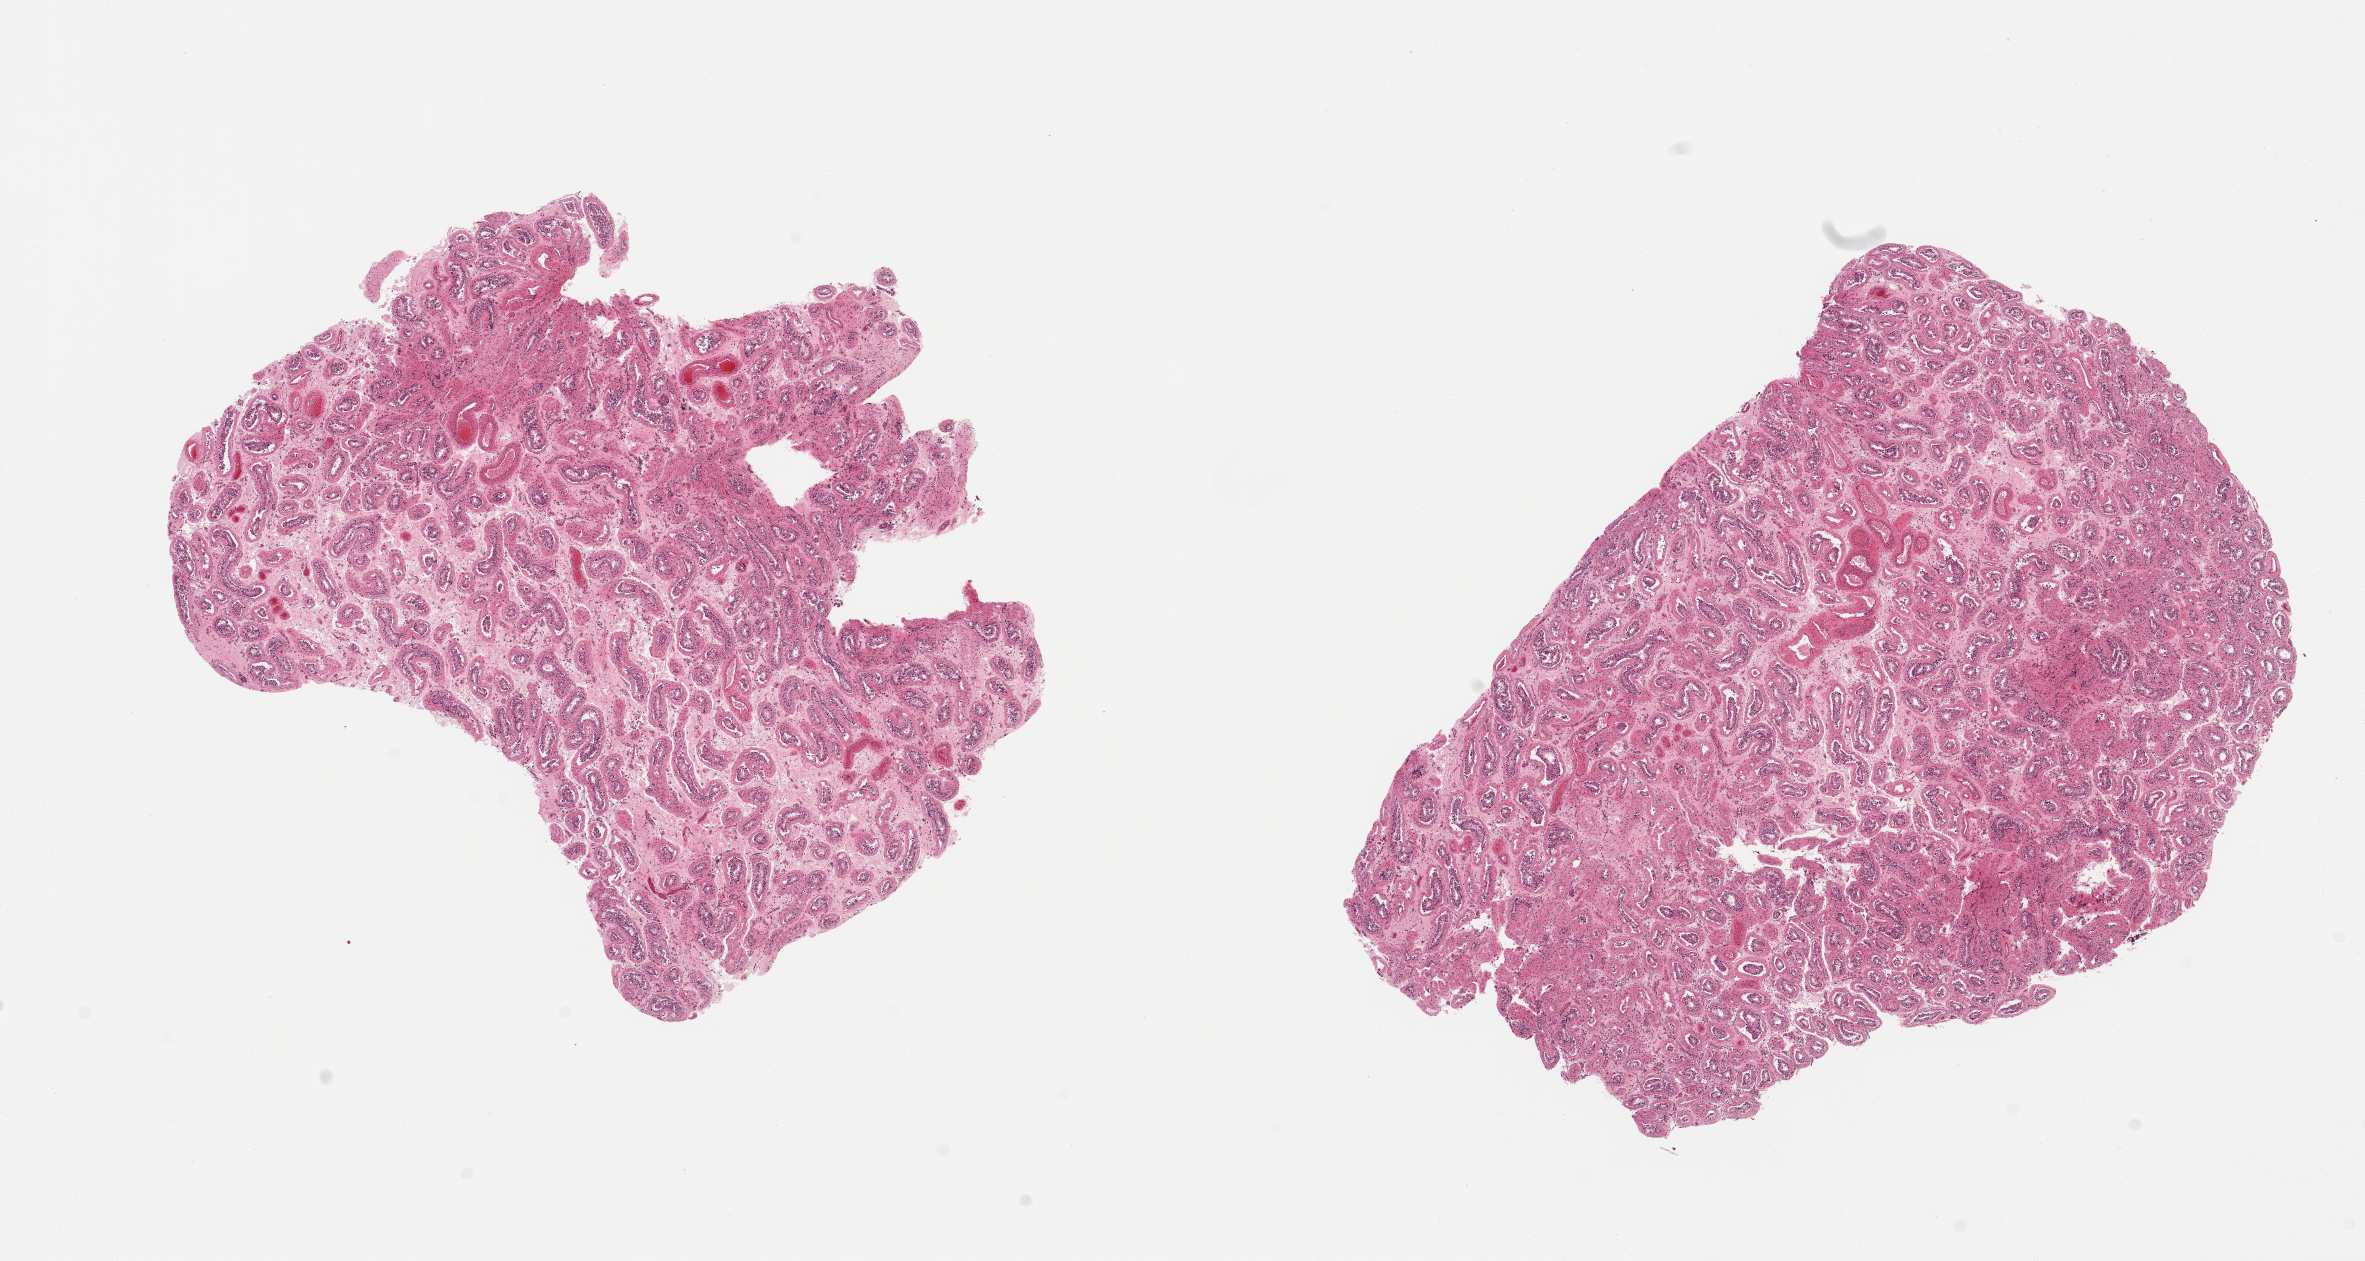
Whole-slide image, H&E stain, a low-resolution overview of the entire scanned area, about 18.7 x 10.0 mm. PAXgene-fixed, paraffin-embedded tissue. Target tissue: testis. Donor tissue sample. Donor: male.
Pathologist's review note for this sample: 2 pieces; atrophy with peritubular fibrosis and some hyalinization, spermatogenesis reduced/absent.